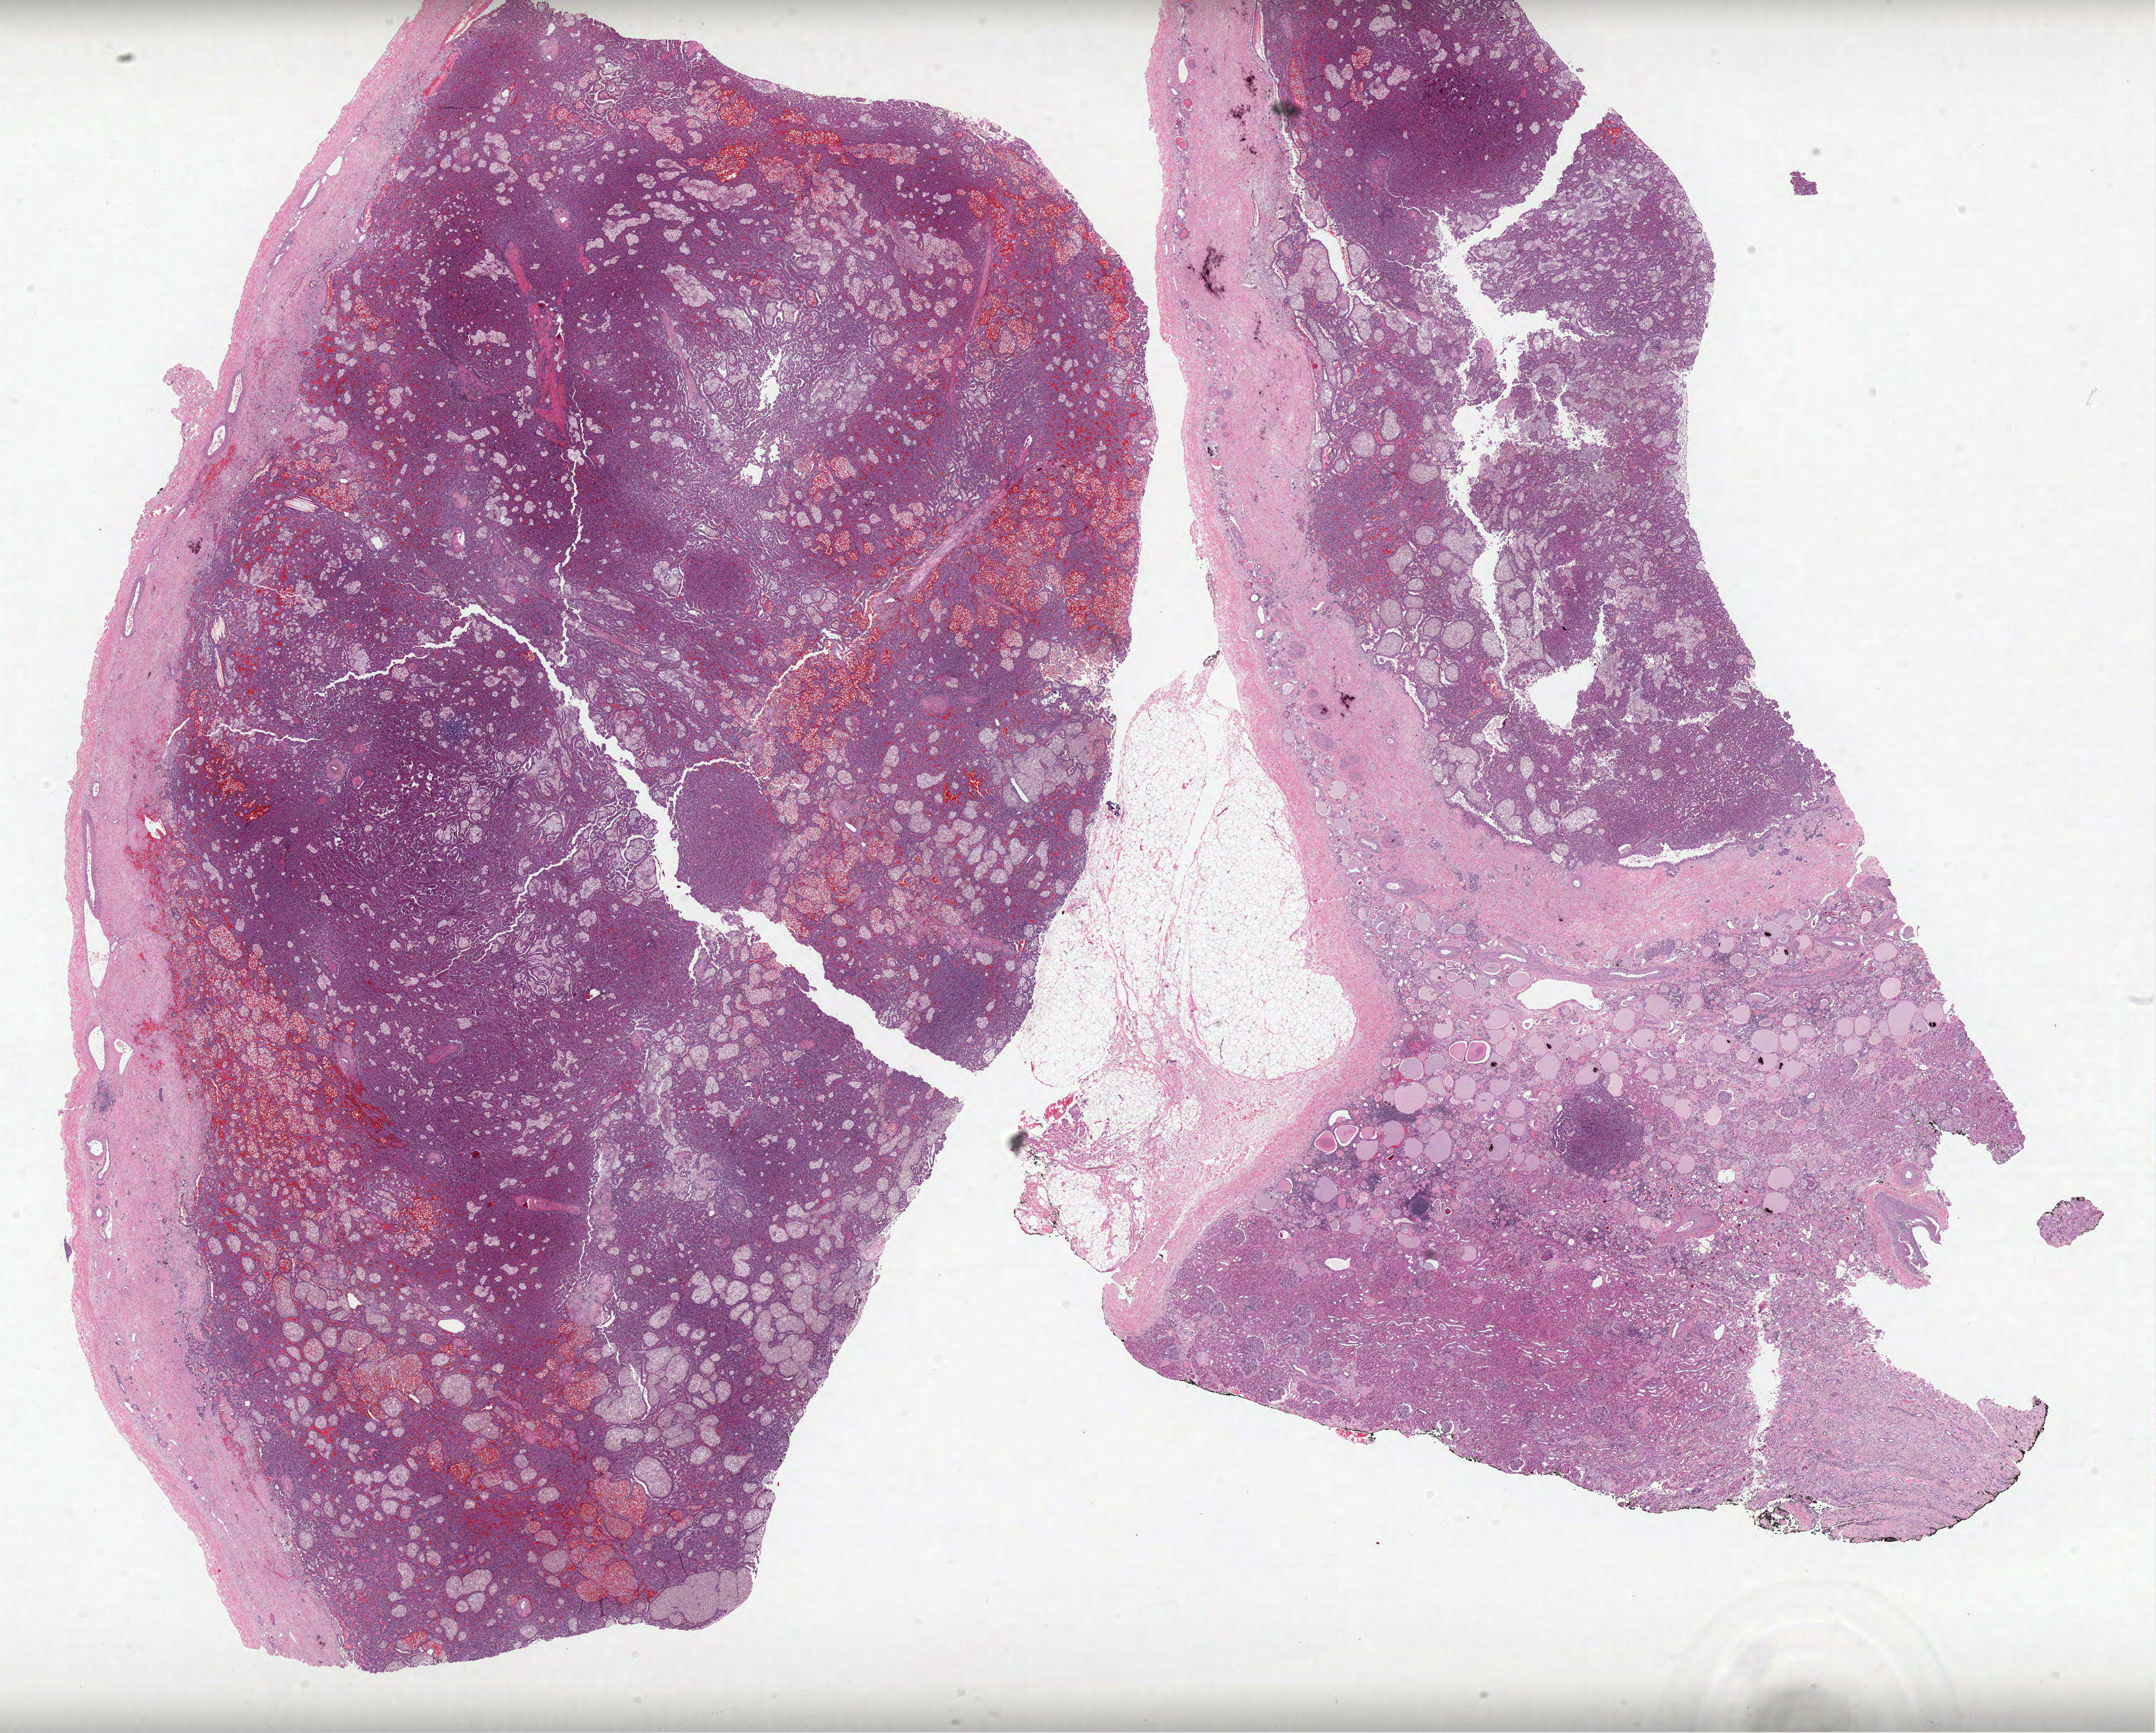
Whole-slide histology image, H&E-stained, shown as a low-resolution overview of the whole scanned area (about 27.6 x 22.2 mm, slide scanned at 40x), formalin-fixed paraffin-embedded (FFPE) diagnostic section, sample: primary tumour, kidney. Patient: male, age at initial diagnosis 64 years.
AJCC pathologic stage: I (7th edition). TNM: T1a NX M0. Pathologic diagnosis: Papillary adenocarcinoma, NOS.